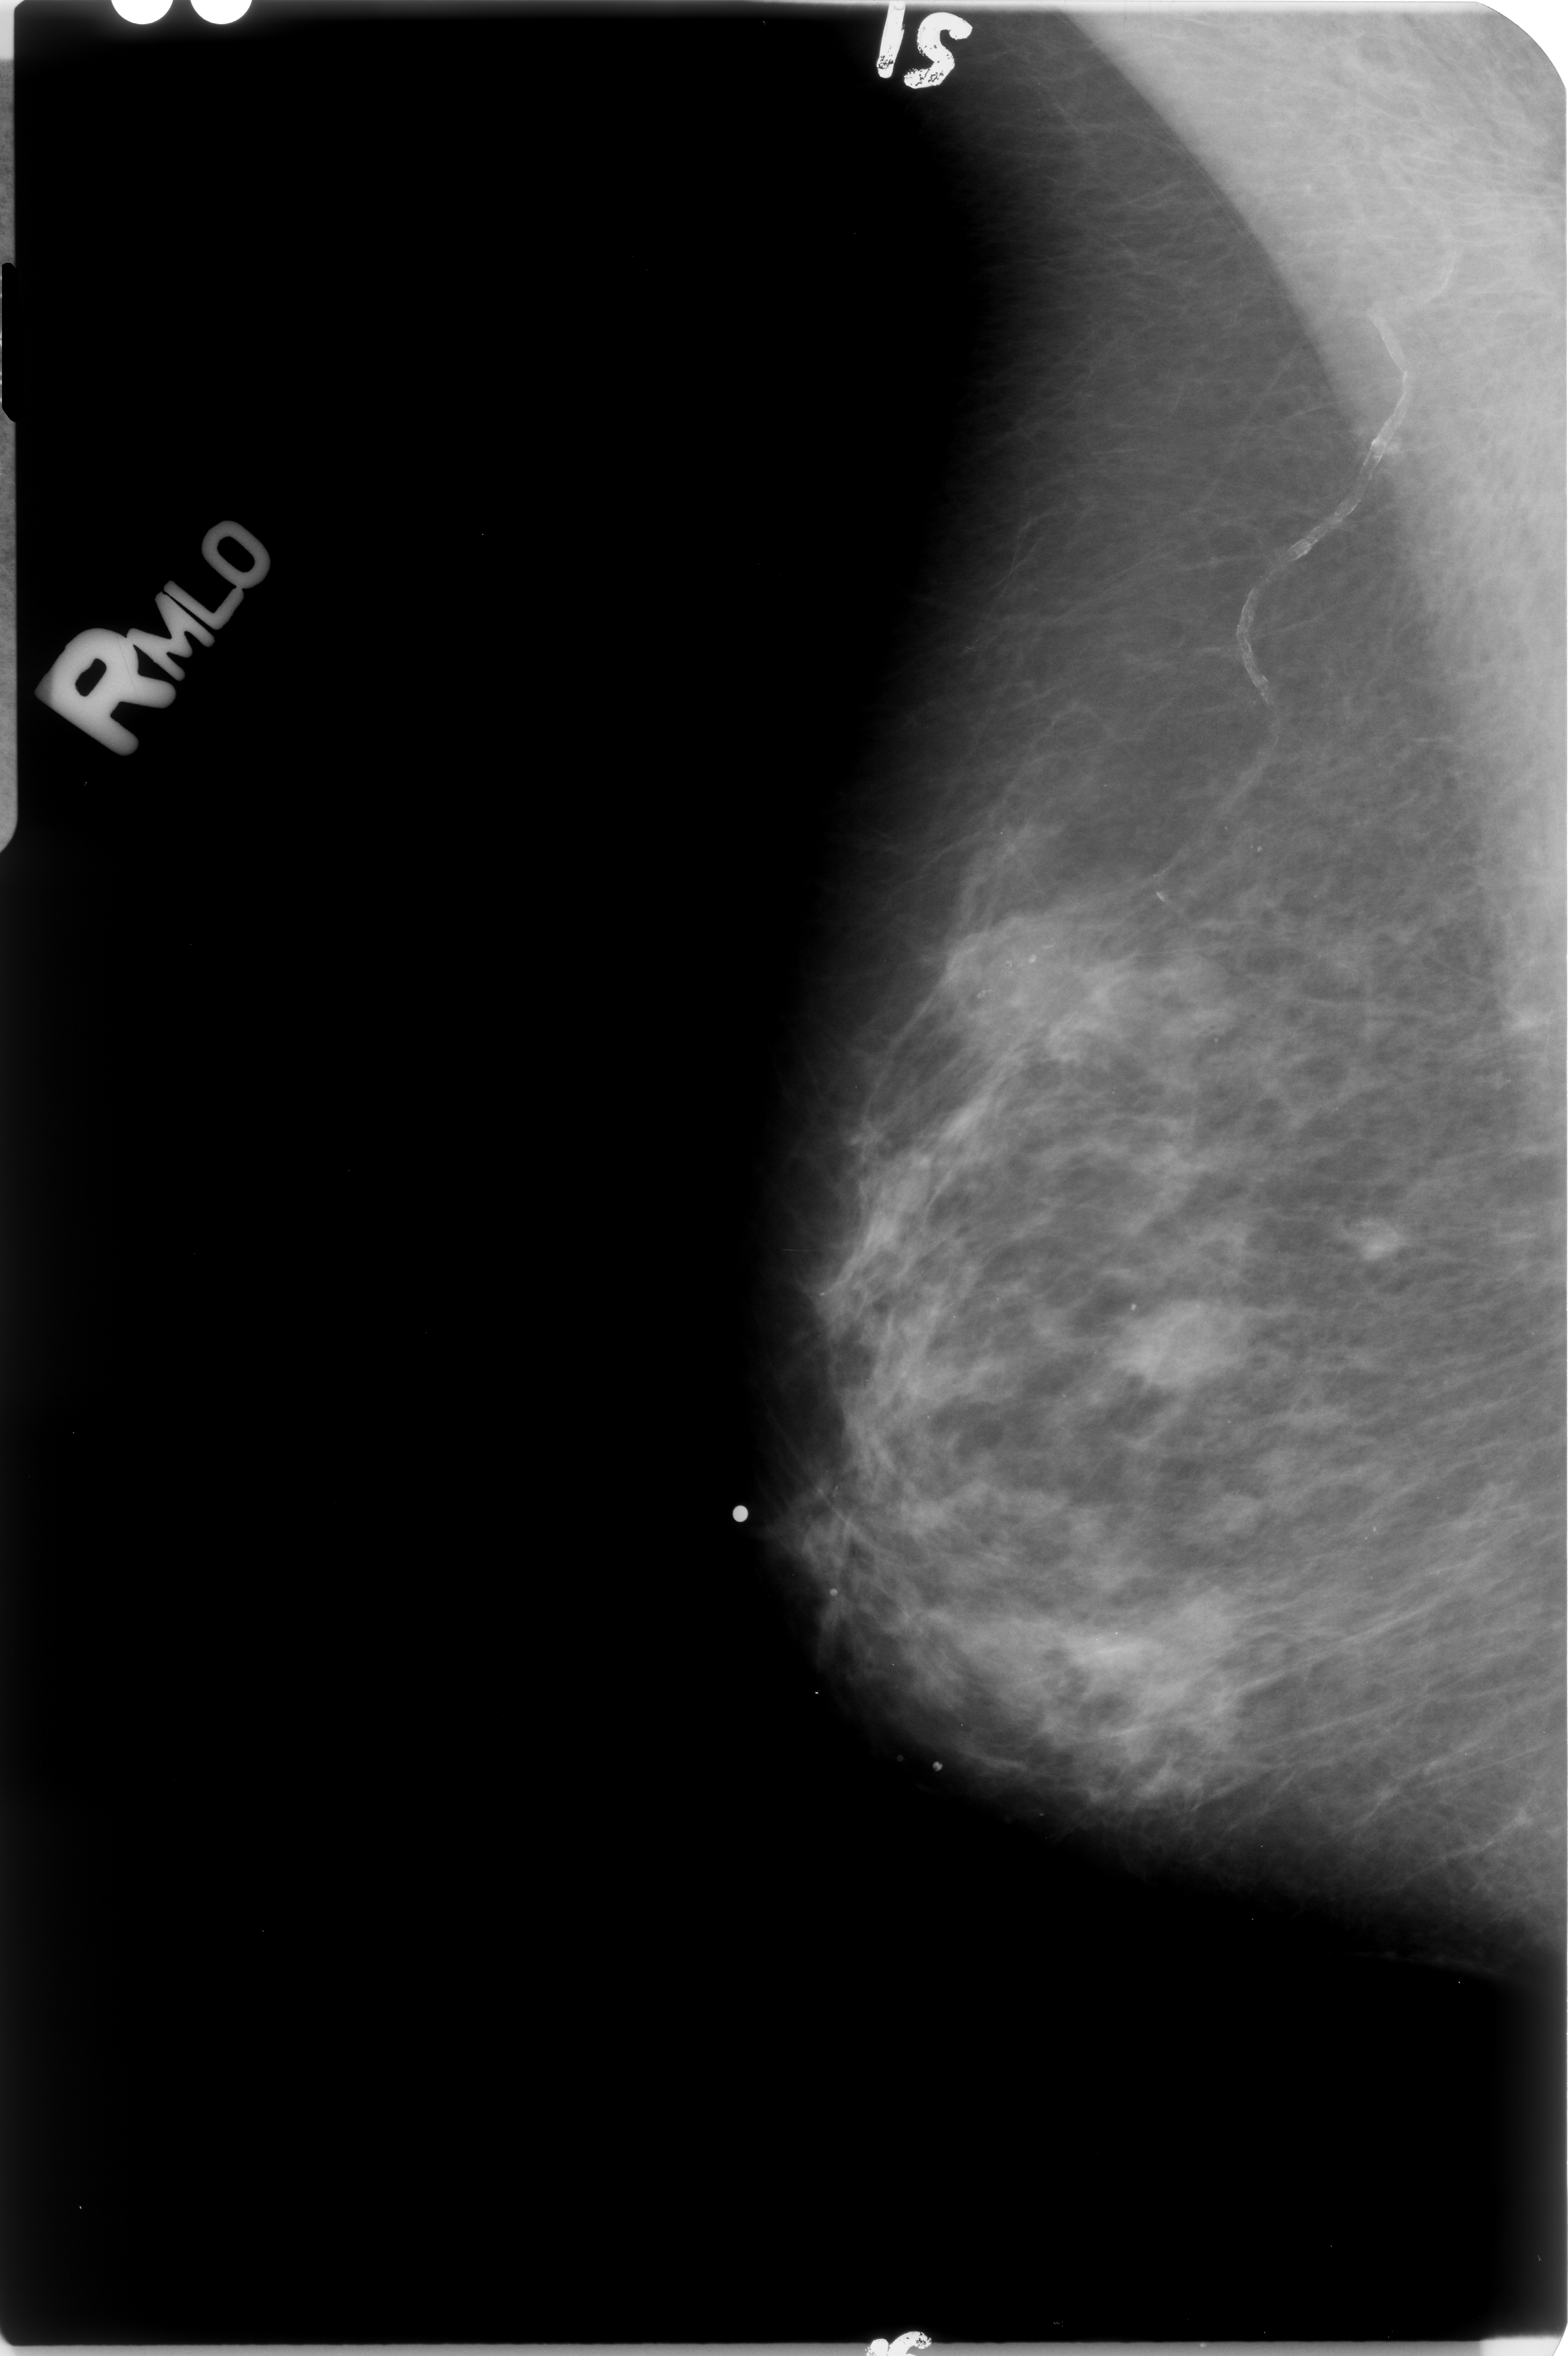
Scanned film-screen mammogram, right breast, MLO view, BI-RADS breast density category 2 (scale 1–4).
Mass; BI-RADS assessment category 0 (incomplete: needs additional imaging); pathology result (as recorded, not read from the image): benign.